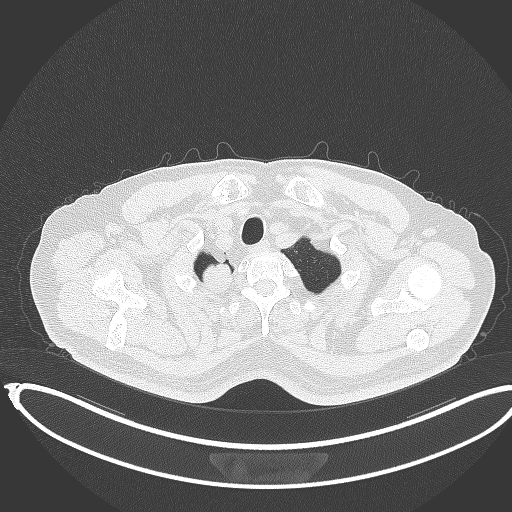
Chest CT, one axial slice; slice 343 of 403 in the series (ordered by position); lung window (W 1500 / L -600 HU); 1 mm slice thickness; 512 × 512 image matrix. Patient: male, 68 years. Case-level facts recorded for this patient, not image findings: clinical TNM (as recorded): T2a N0 M0.
Outlined on this slice (bounding box drawn by a radiologist):
- lung tumour (recorded histology: adenocarcinoma): bounding box [x1, y1, x2, y2] px = [197, 259, 239, 302]